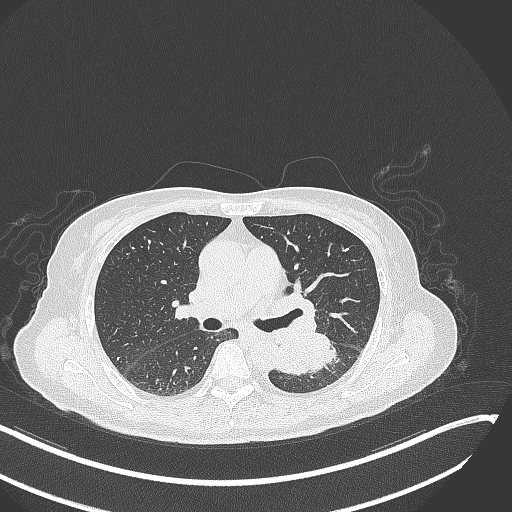
Chest CT, one axial slice. Slice 164 of 342 in the series (ordered by position). Lung window (W 1500 / L -600 HU). 1 mm slice thickness. 512 × 512 image matrix. Female patient, age 64 years. From the clinical record (not read from this slice): clinical TNM (as recorded): T3 N1 M1; histopathological grade: G3.
Annotated regions visible in this slice (rectangle marked by the reading radiologist):
- lung tumour (recorded histology: small cell carcinoma): bounding box <272,335,342,376> (left, top, right, bottom; pixels)